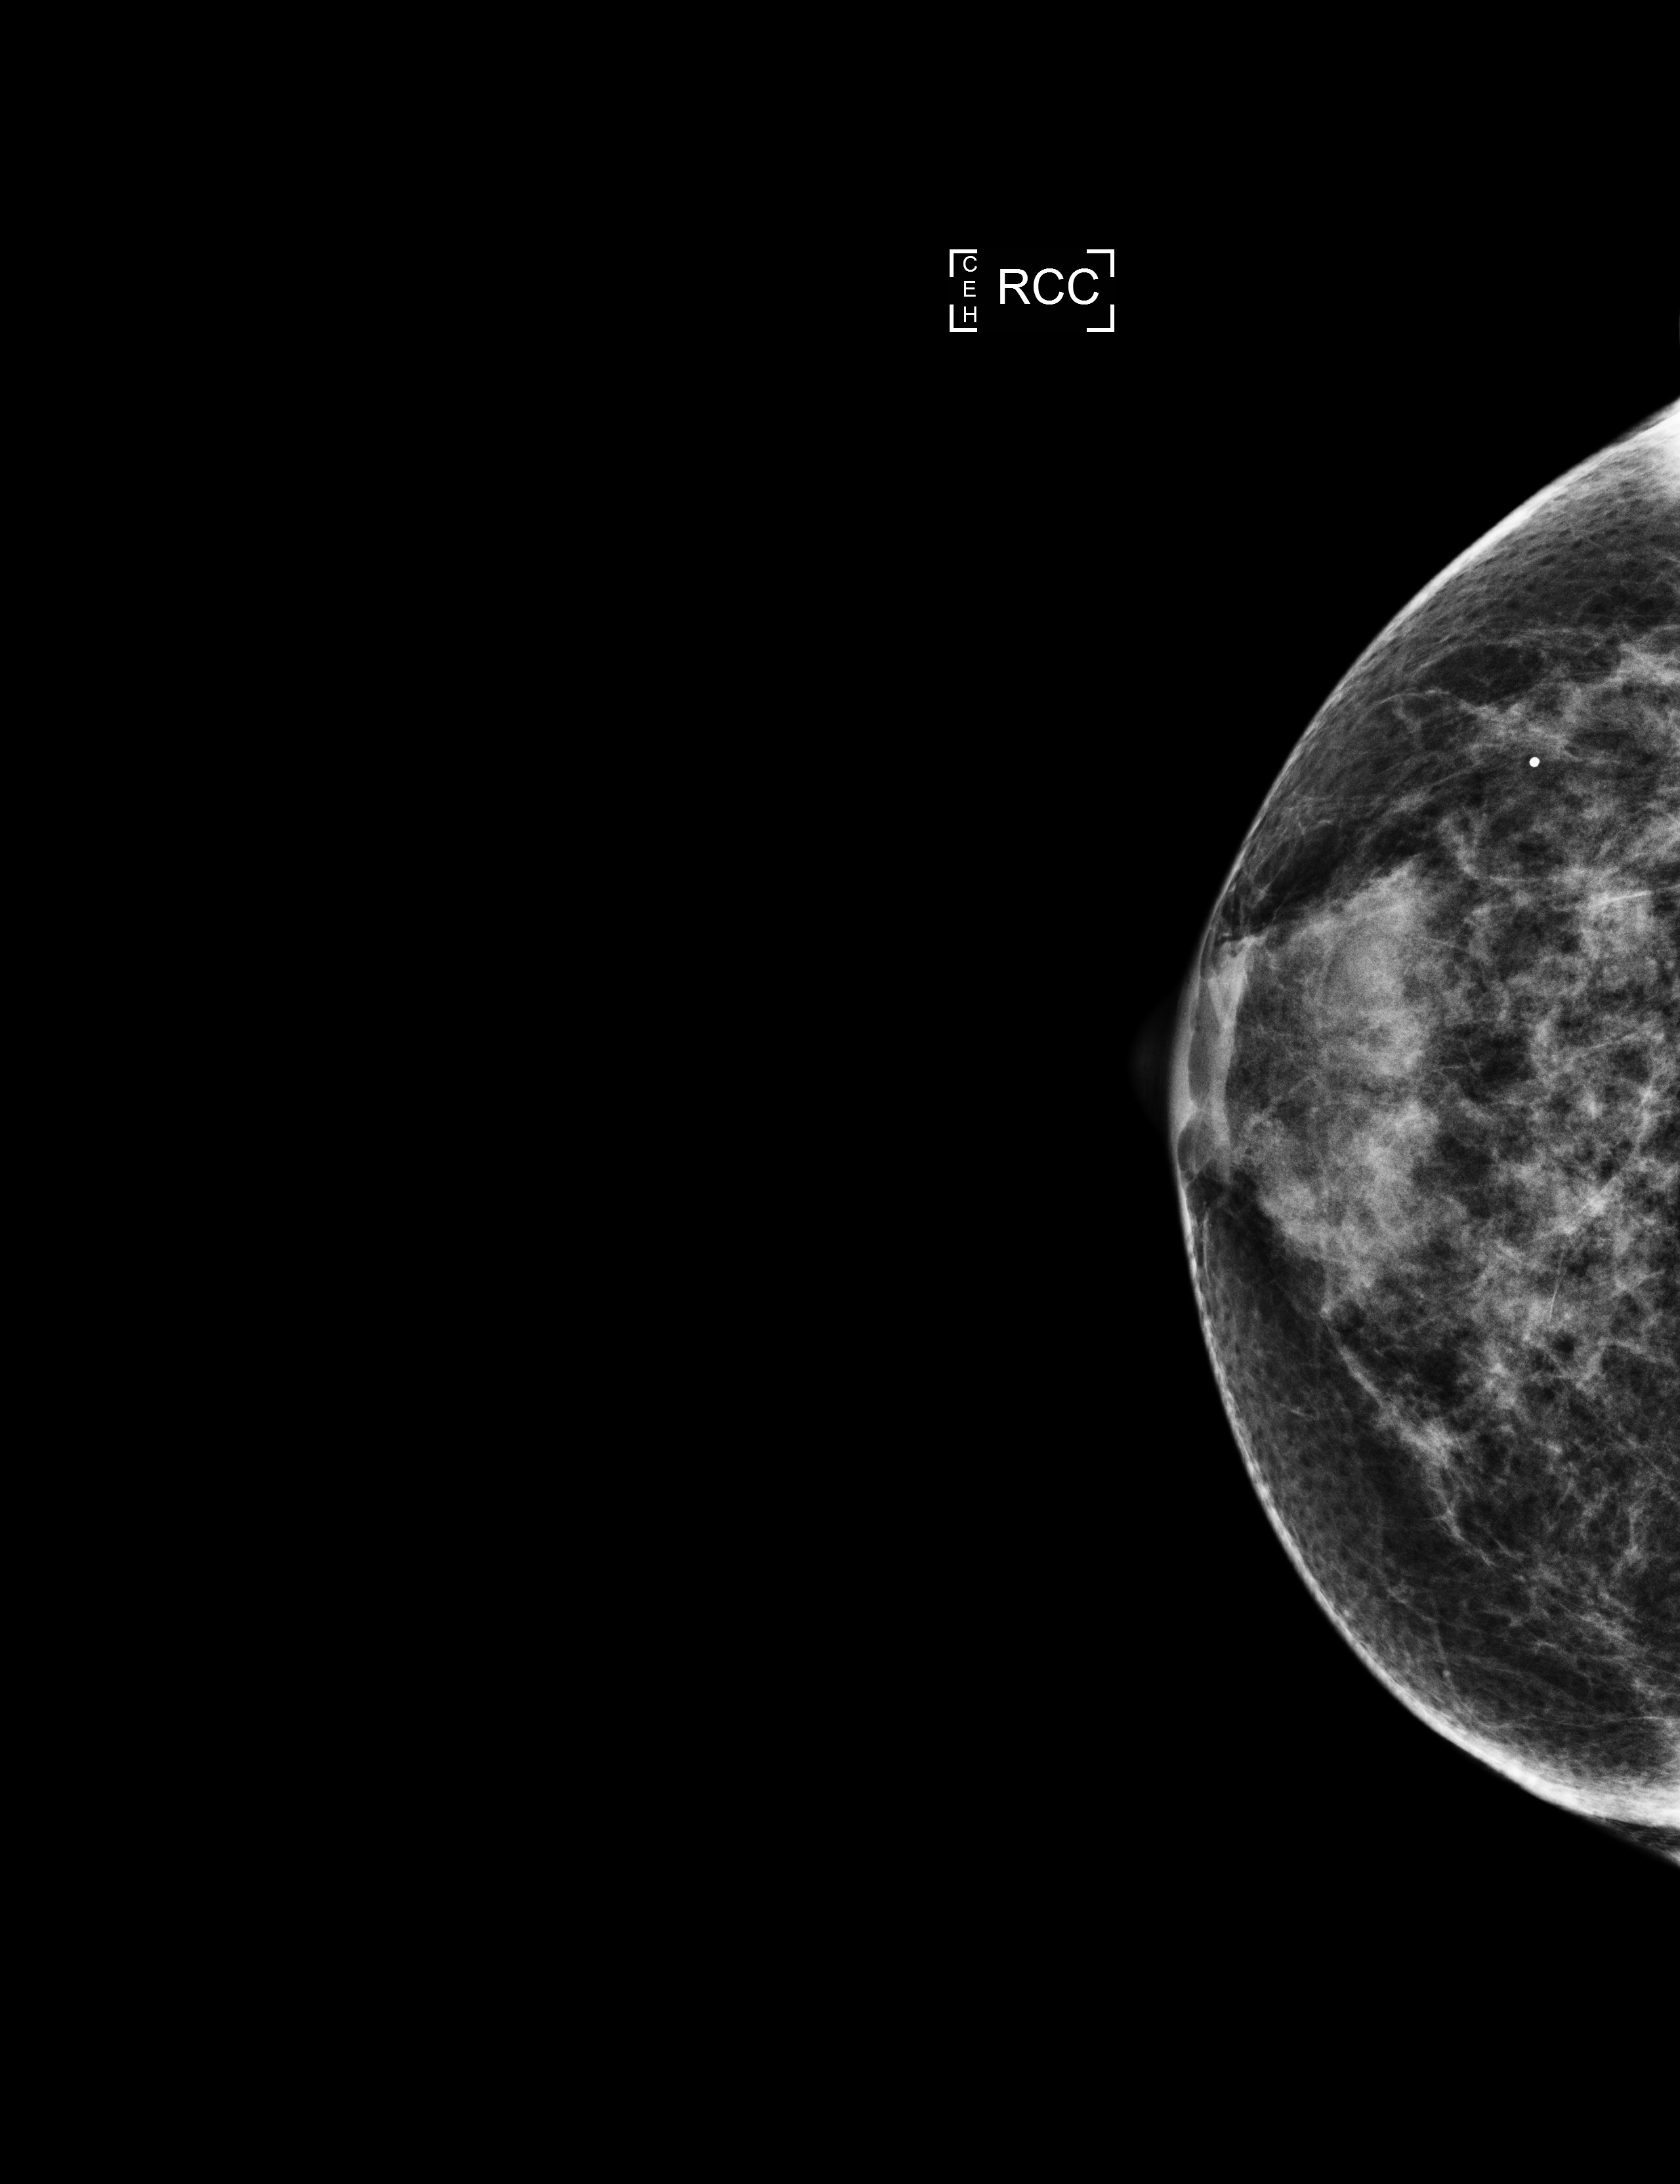
Annual screening mammography examination, compressed breast thickness 45 mm, system: Selenia Dimensions. Patient aged 60 years (female).
Image type: full-field digital mammogram. Breast: right. Projection: CC view.